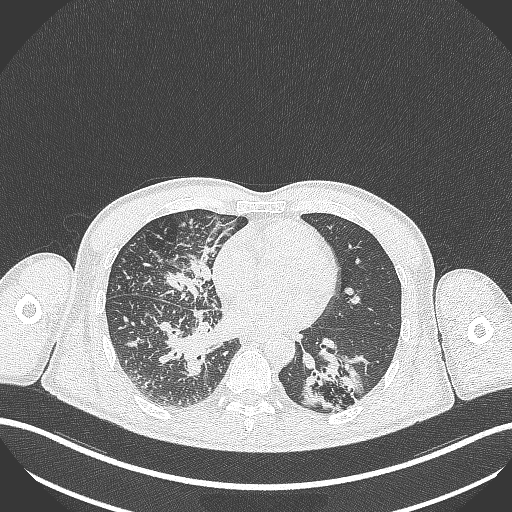
Chest CT, one axial slice. Slice 132 of 348 in the series (ordered by position). Lung window (W 1500 / L -600 HU). 1 mm slice thickness. 512 × 512 image matrix, field of view 400 × 400 mm. Patient: male, 49 years. Case-level facts recorded for this patient, not image findings: clinical TNM (as recorded): T2b N1 M0.
Outlined on this slice (rectangle marked by the reading radiologist):
- lung tumour (recorded histology: adenocarcinoma): bounding box [x1, y1, x2, y2] px = [299, 351, 371, 419]